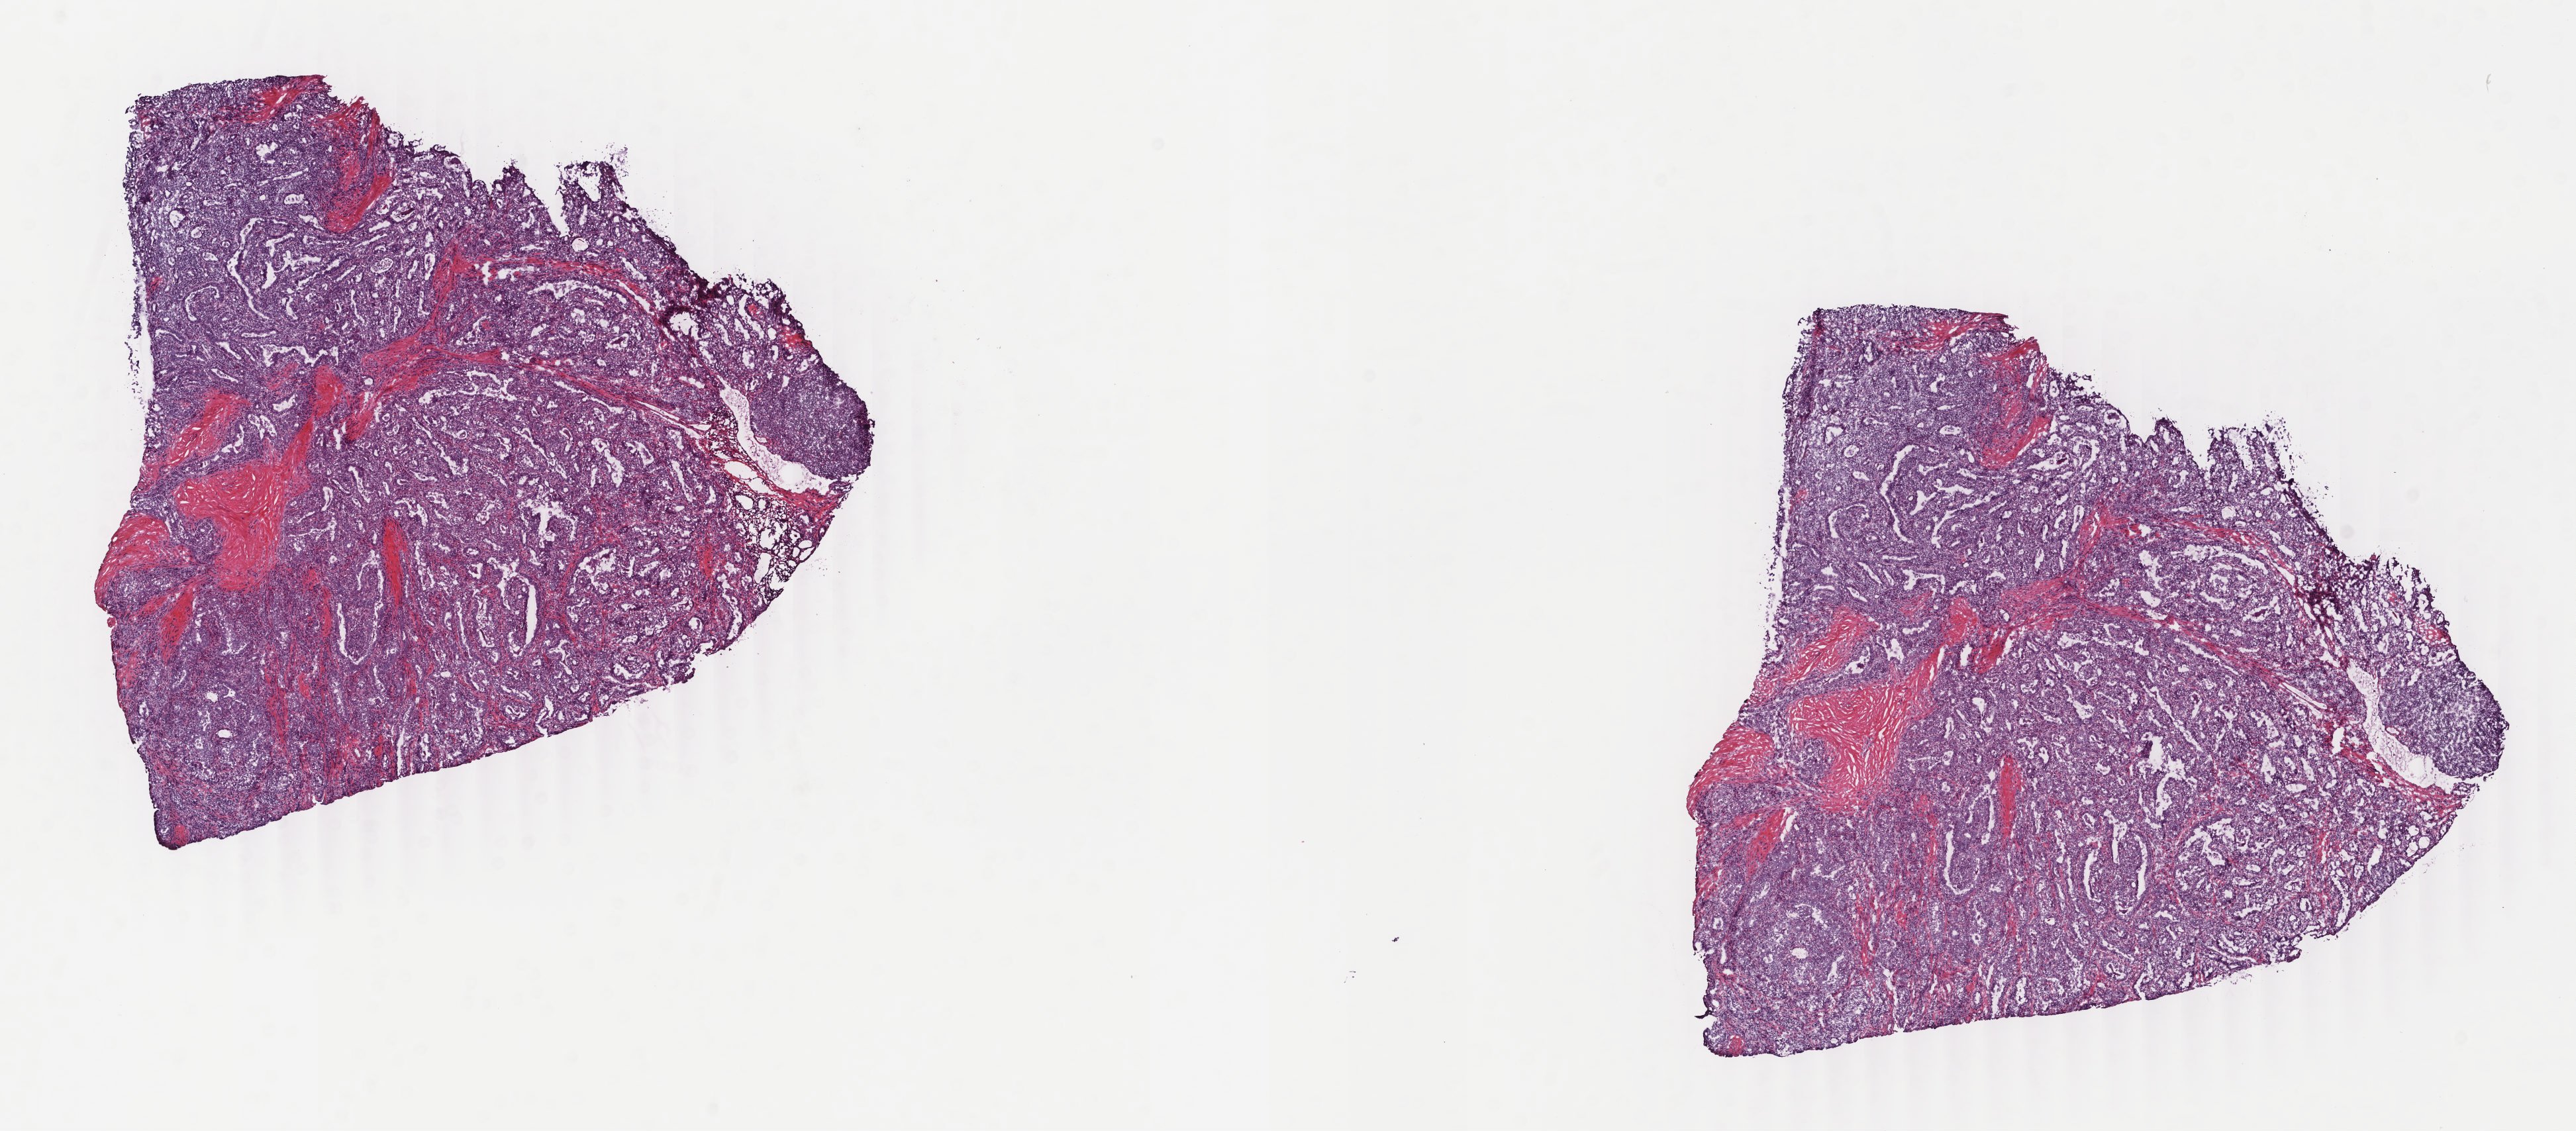
Whole-slide histology image, Hematoxylin and eosin (H&E) stained, a low-resolution overview of the entire scanned area, about 15.5 x 6.8 mm (slide scanned at 40x), frozen section, sample: primary tumour, thyroid. Male, age 52 years at initial diagnosis. Composition of this section per pathologist review: tumour cells 100%, tumour nuclei 78%, normal cells 0%, stromal cells 0%, necrosis 0%. Inflammatory infiltration, as recorded: lymphocyte infiltration 0%, monocyte infiltration 0%, neutrophil infiltration 0%.
• TNM: T1b N0 MX
• laterality: right
• pathologic diagnosis: Papillary adenocarcinoma, NOS (thyroid gland)
• AJCC pathologic stage: I (7th edition)